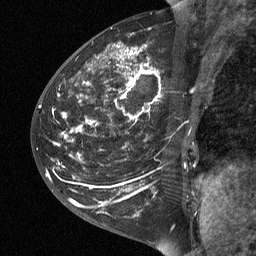
Breast MRI (dynamic contrast-enhanced), one sagittal slice; slice 25 of 64 in the series (ordered by position); dynamic contrast-enhanced study with each time point stored as its own series, time point 2 of 3 at this slice position (early post-contrast, ordered by acquisition time); 1.5 T; TE 4.8 ms, TR 27 ms; 2 mm slice thickness; 256 × 256 image matrix. Patient: female, 42 years. From the clinical record (not read from this slice): setting: breast cancer imaged before/during neoadjuvant chemotherapy; receptor status: triple-negative.
Structures marked on this image (semi-automatic segmentation, software-assisted and operator-edited):
- analysis volume of interest (the breast-tissue region the enhancement analysis was run in; not a lesion): bounding box [x1, y1, x2, y2] px = [43, 29, 203, 190]
- tumour enhancement mask (voxels above the 90 % enhancement threshold inside the analysis volume of interest): [80, 46, 150, 131]